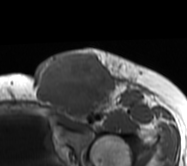
MRI of an extremity soft-tissue mass, one axial slice; position 39 of 62 along the scan axis; MR volume resampled by the dataset authors to the PET/CT grid (not the native acquisition matrix); 187 × 166 image matrix, field of view 183 × 162 mm. Female patient. Case-level facts recorded for this patient, not image findings: histological type: leiomyosarcoma; grade: high; site of the primary tumour: groin.
Outlined on this slice (expert contour drawn on MRI and transferred to this co-registered scan by the dataset authors):
- gross tumour volume including surrounding oedema: bounding box [x1, y1, x2, y2] px = [34, 47, 149, 123]
- gross tumour volume (mass): [34, 51, 115, 120]